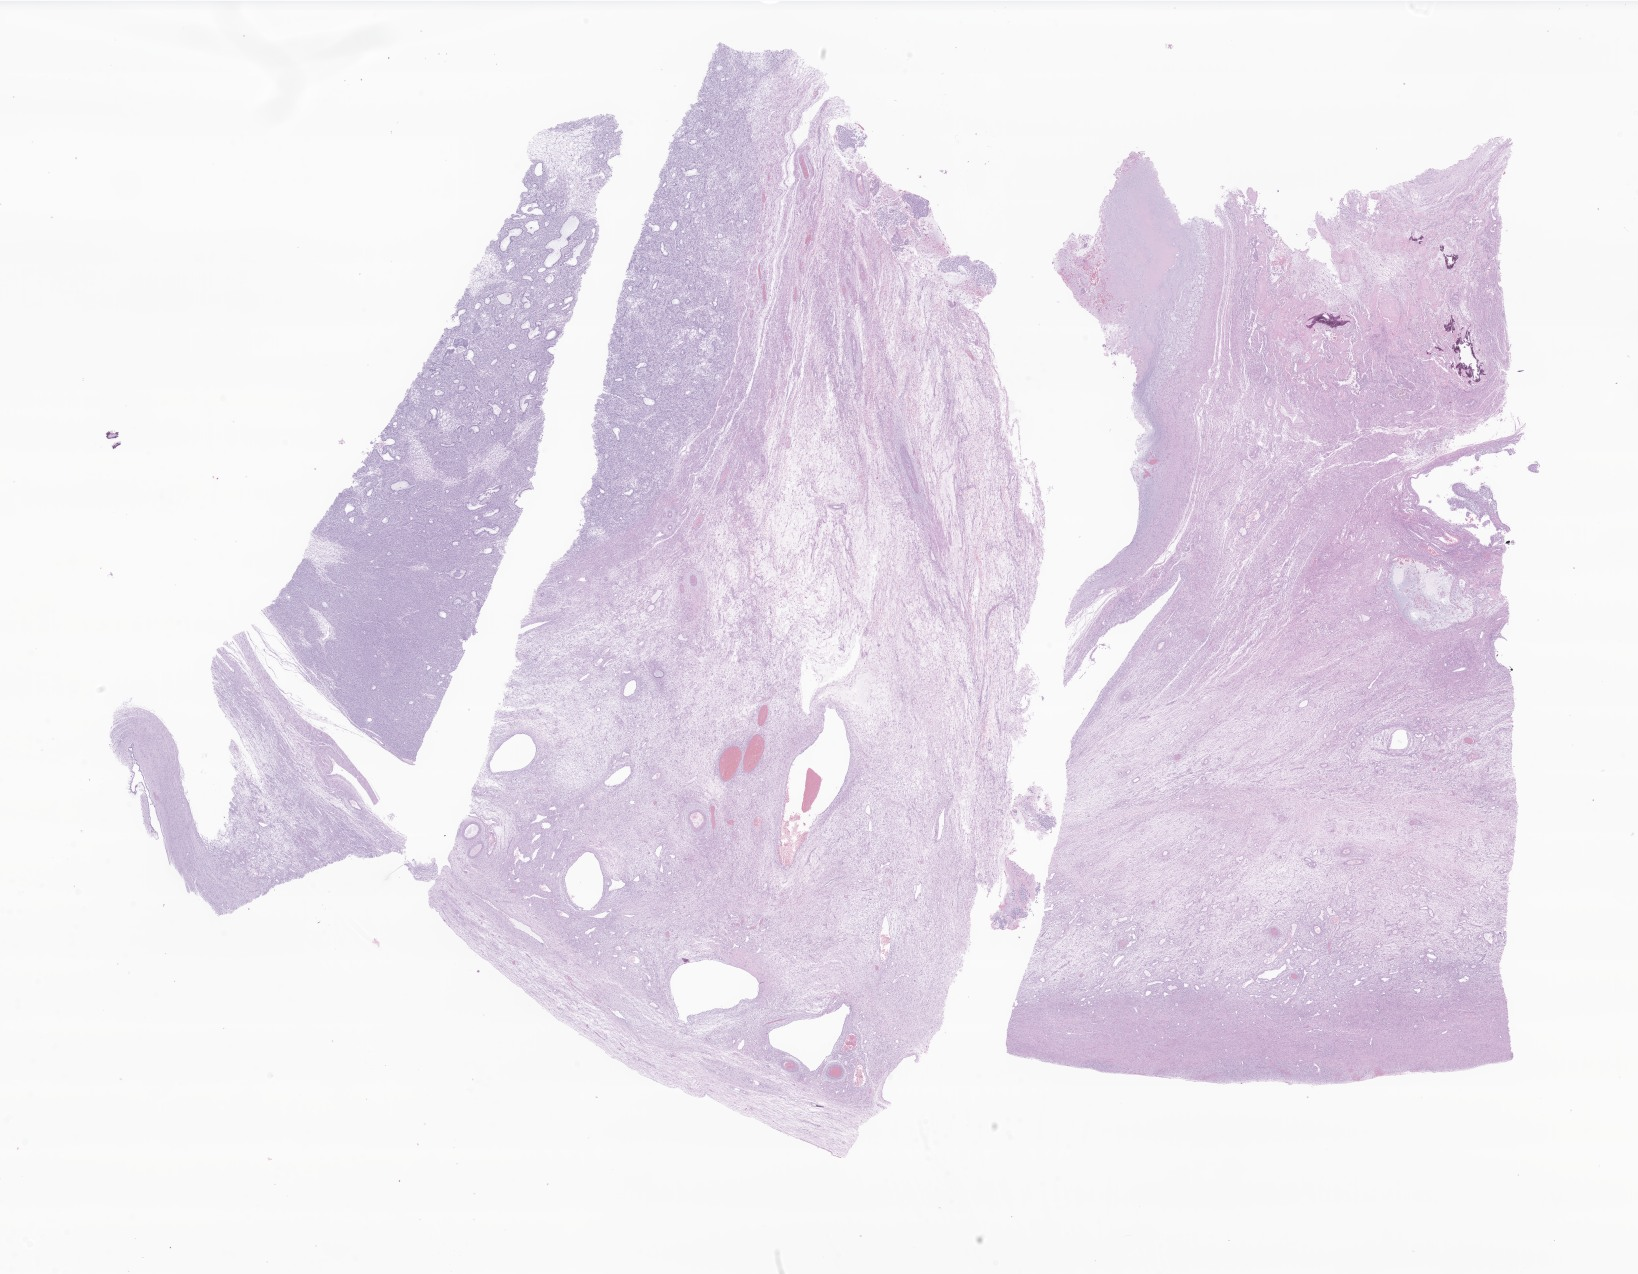
H&E whole-slide image of tumor tissue from the ovary — shown as a low-resolution overview of the whole scanned area (about 27.6 x 21.5 mm). Formalin-fixed paraffin-embedded section. Patient: female, age 215 months (17 years 11 months).
Diagnosis (ICD-O-3 morphology term): Adult granulosa cell tumor of ovary.